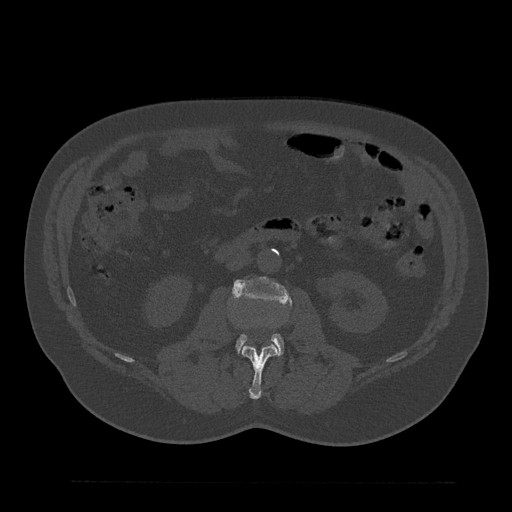
CT including the spine, one axial slice. Slice 69 of 797 in the series (ordered by position). Reconstruction kernel Br40s/3. 120 kVp. Bone window (W 1800 / L 400 HU). 0.5 mm slice thickness. 512 × 512 image matrix. Patient: male, 61 years. From the clinical record (not read from this slice): primary cancer: prostate.
Annotated regions visible in this slice (semi-automatic segmentation, software-assisted and operator-edited):
- L2 vertebra: bounding box (x1, y1, x2, y2) in pixels: (241, 345, 279, 399)
- L3 vertebra: (233, 277, 292, 354)